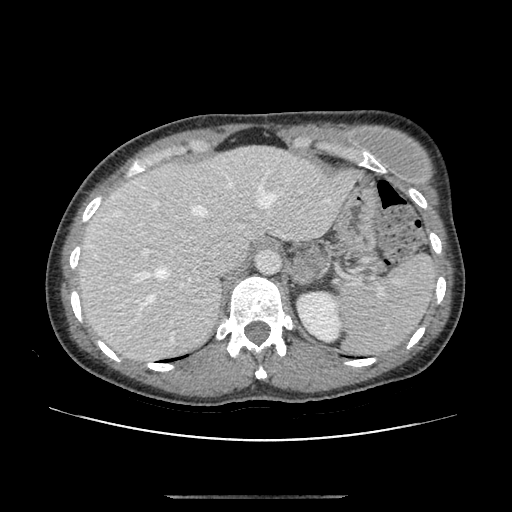
Contrast-enhanced abdominal CT, one axial slice. Reconstruction kernel STANDARD. 120 kVp. Soft-tissue window (W 400 / L 40 HU). 512 × 512 image matrix. Patient: female, 51 years. From the clinical record (not read from this slice): diagnosis: adrenocortical carcinoma; tumour side: left adrenal; tumour size at pathology: 3.5 cm; Ki-67 index: 45 %; stage (as recorded): 1.
Annotated regions visible in this slice (semi-automatic segmentation, software-assisted and operator-edited):
- mass: box from (x=291, y=248) to (x=324, y=284) px